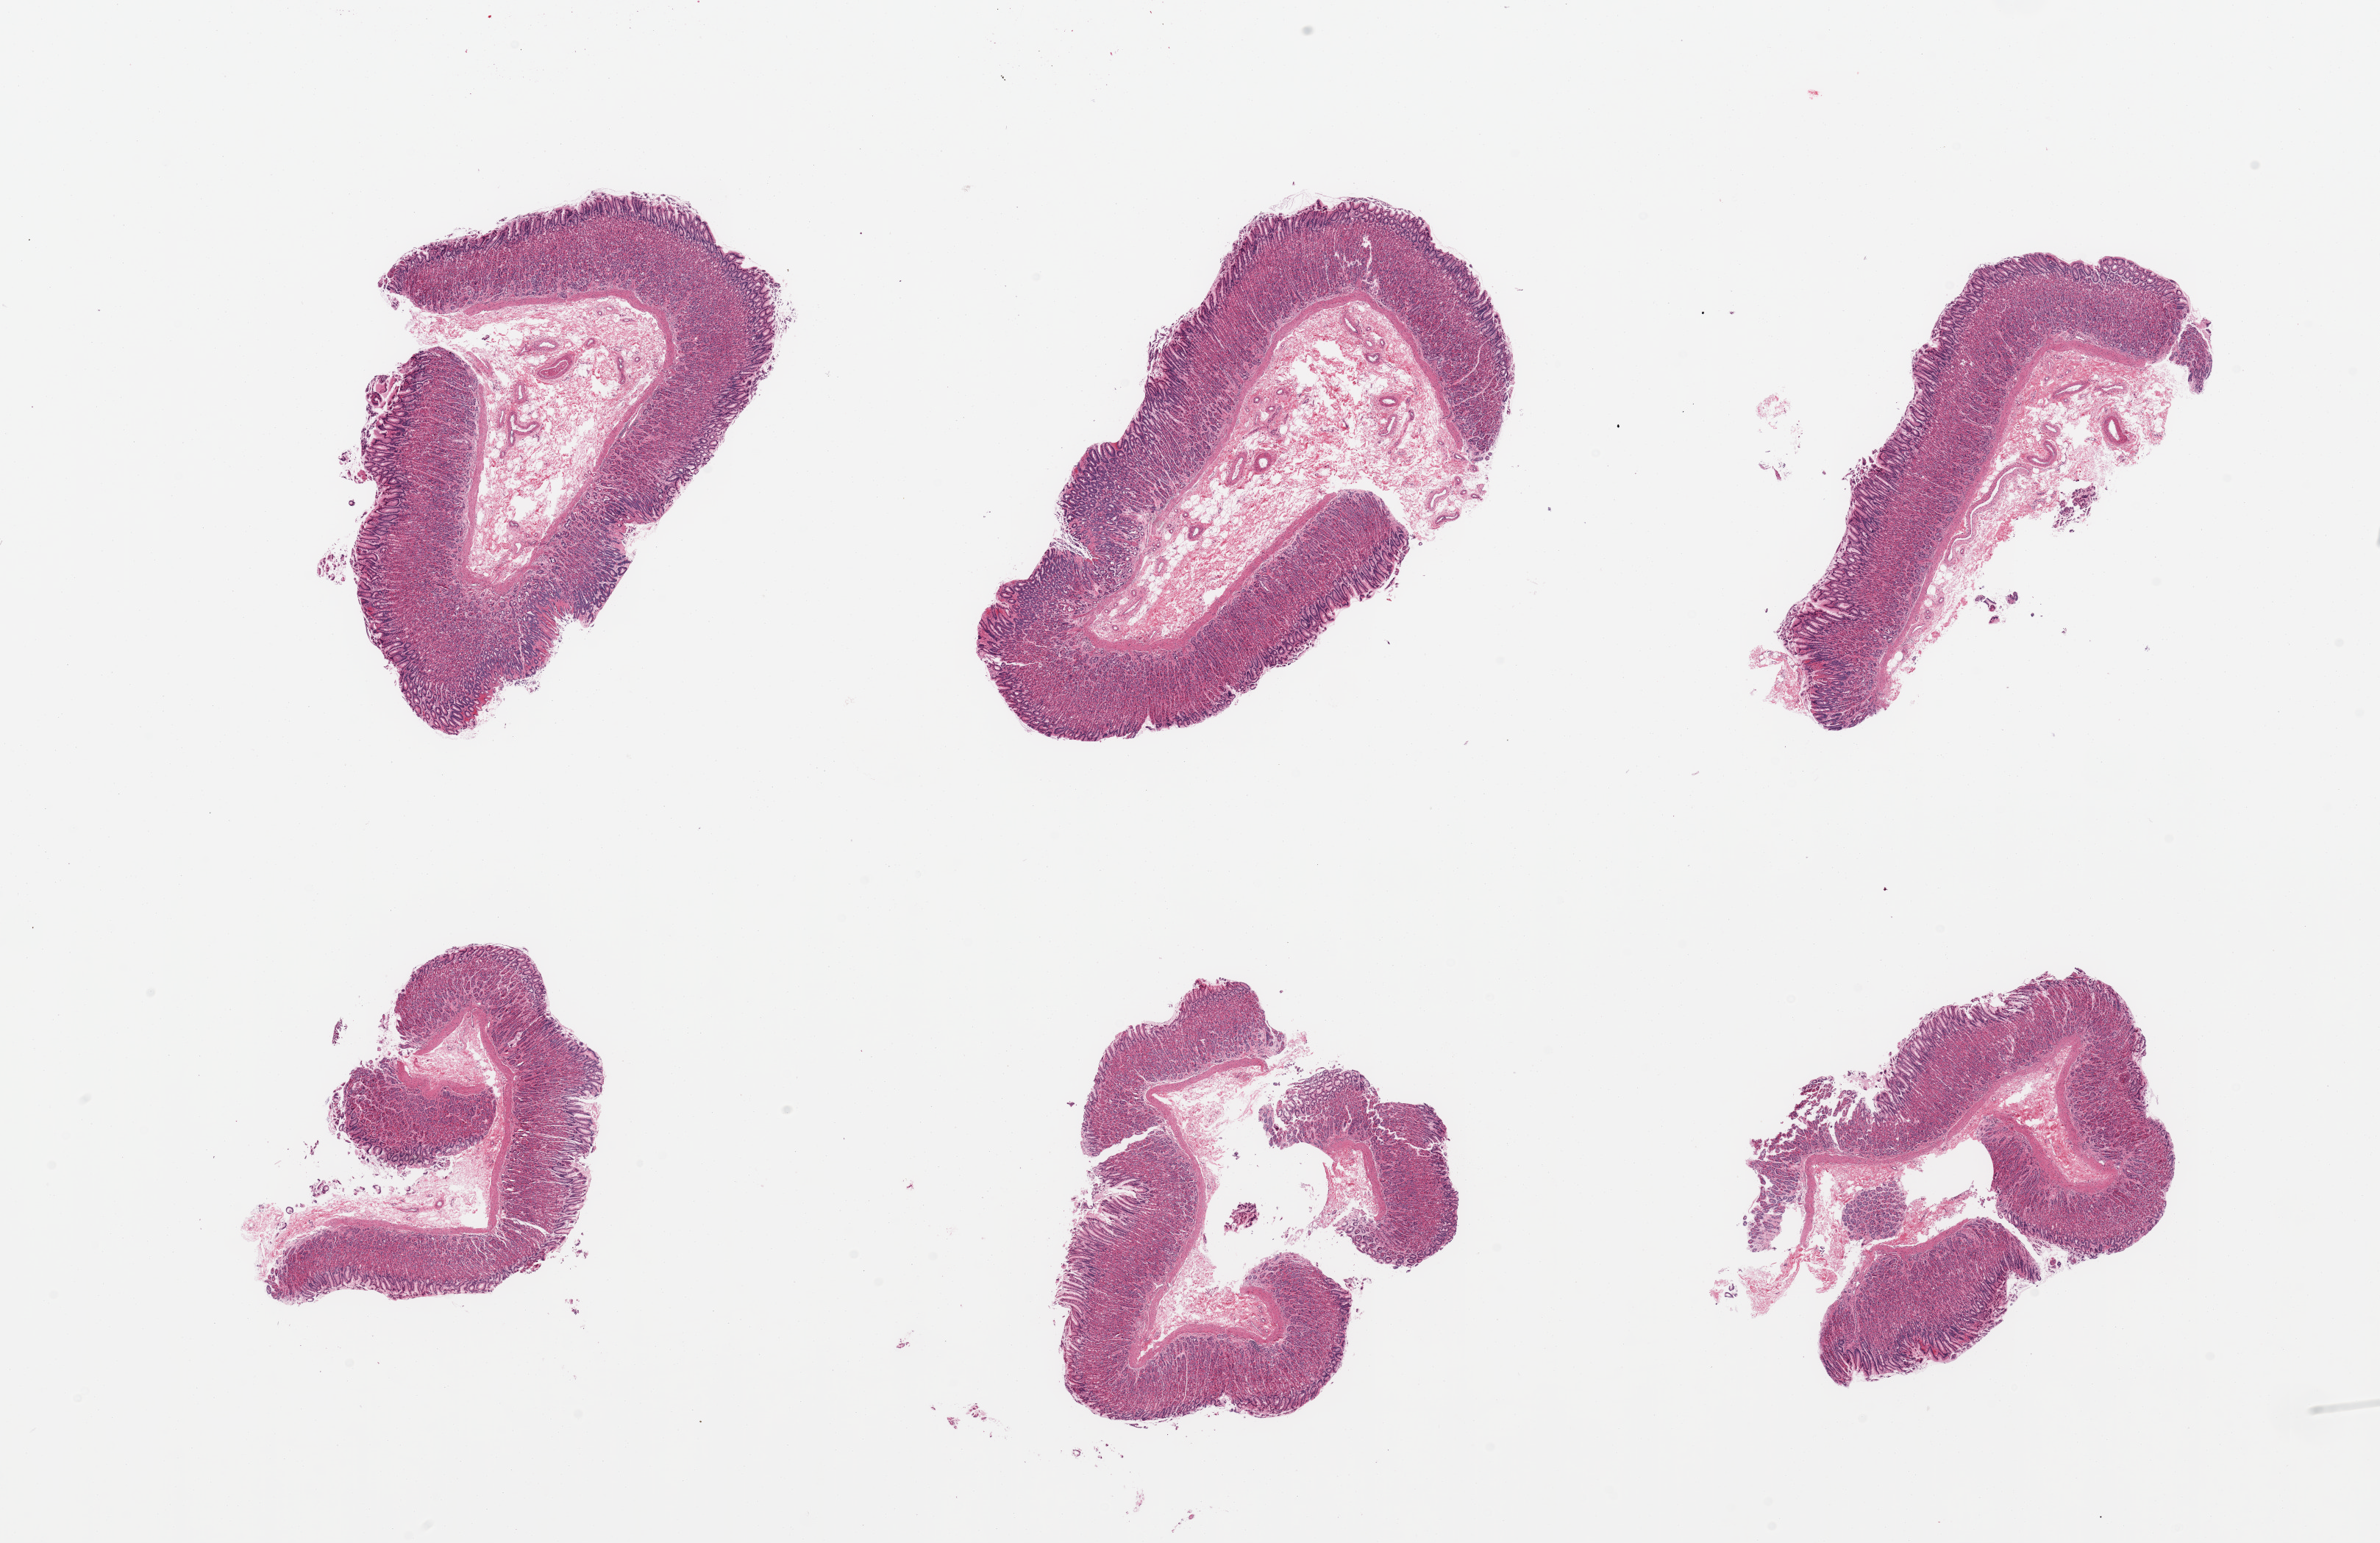
Whole-slide image, haematoxylin and eosin stain — a low-resolution overview of the entire scanned area, about 25.6 x 16.6 mm; PAXgene-fixed paraffin-embedded (PFPE) section; section of stomach (target tissue); tissue donor sample. Male donor.
Review note (as recorded): 6 pieces; well preserved mucosa and submucosa, no muscularis.